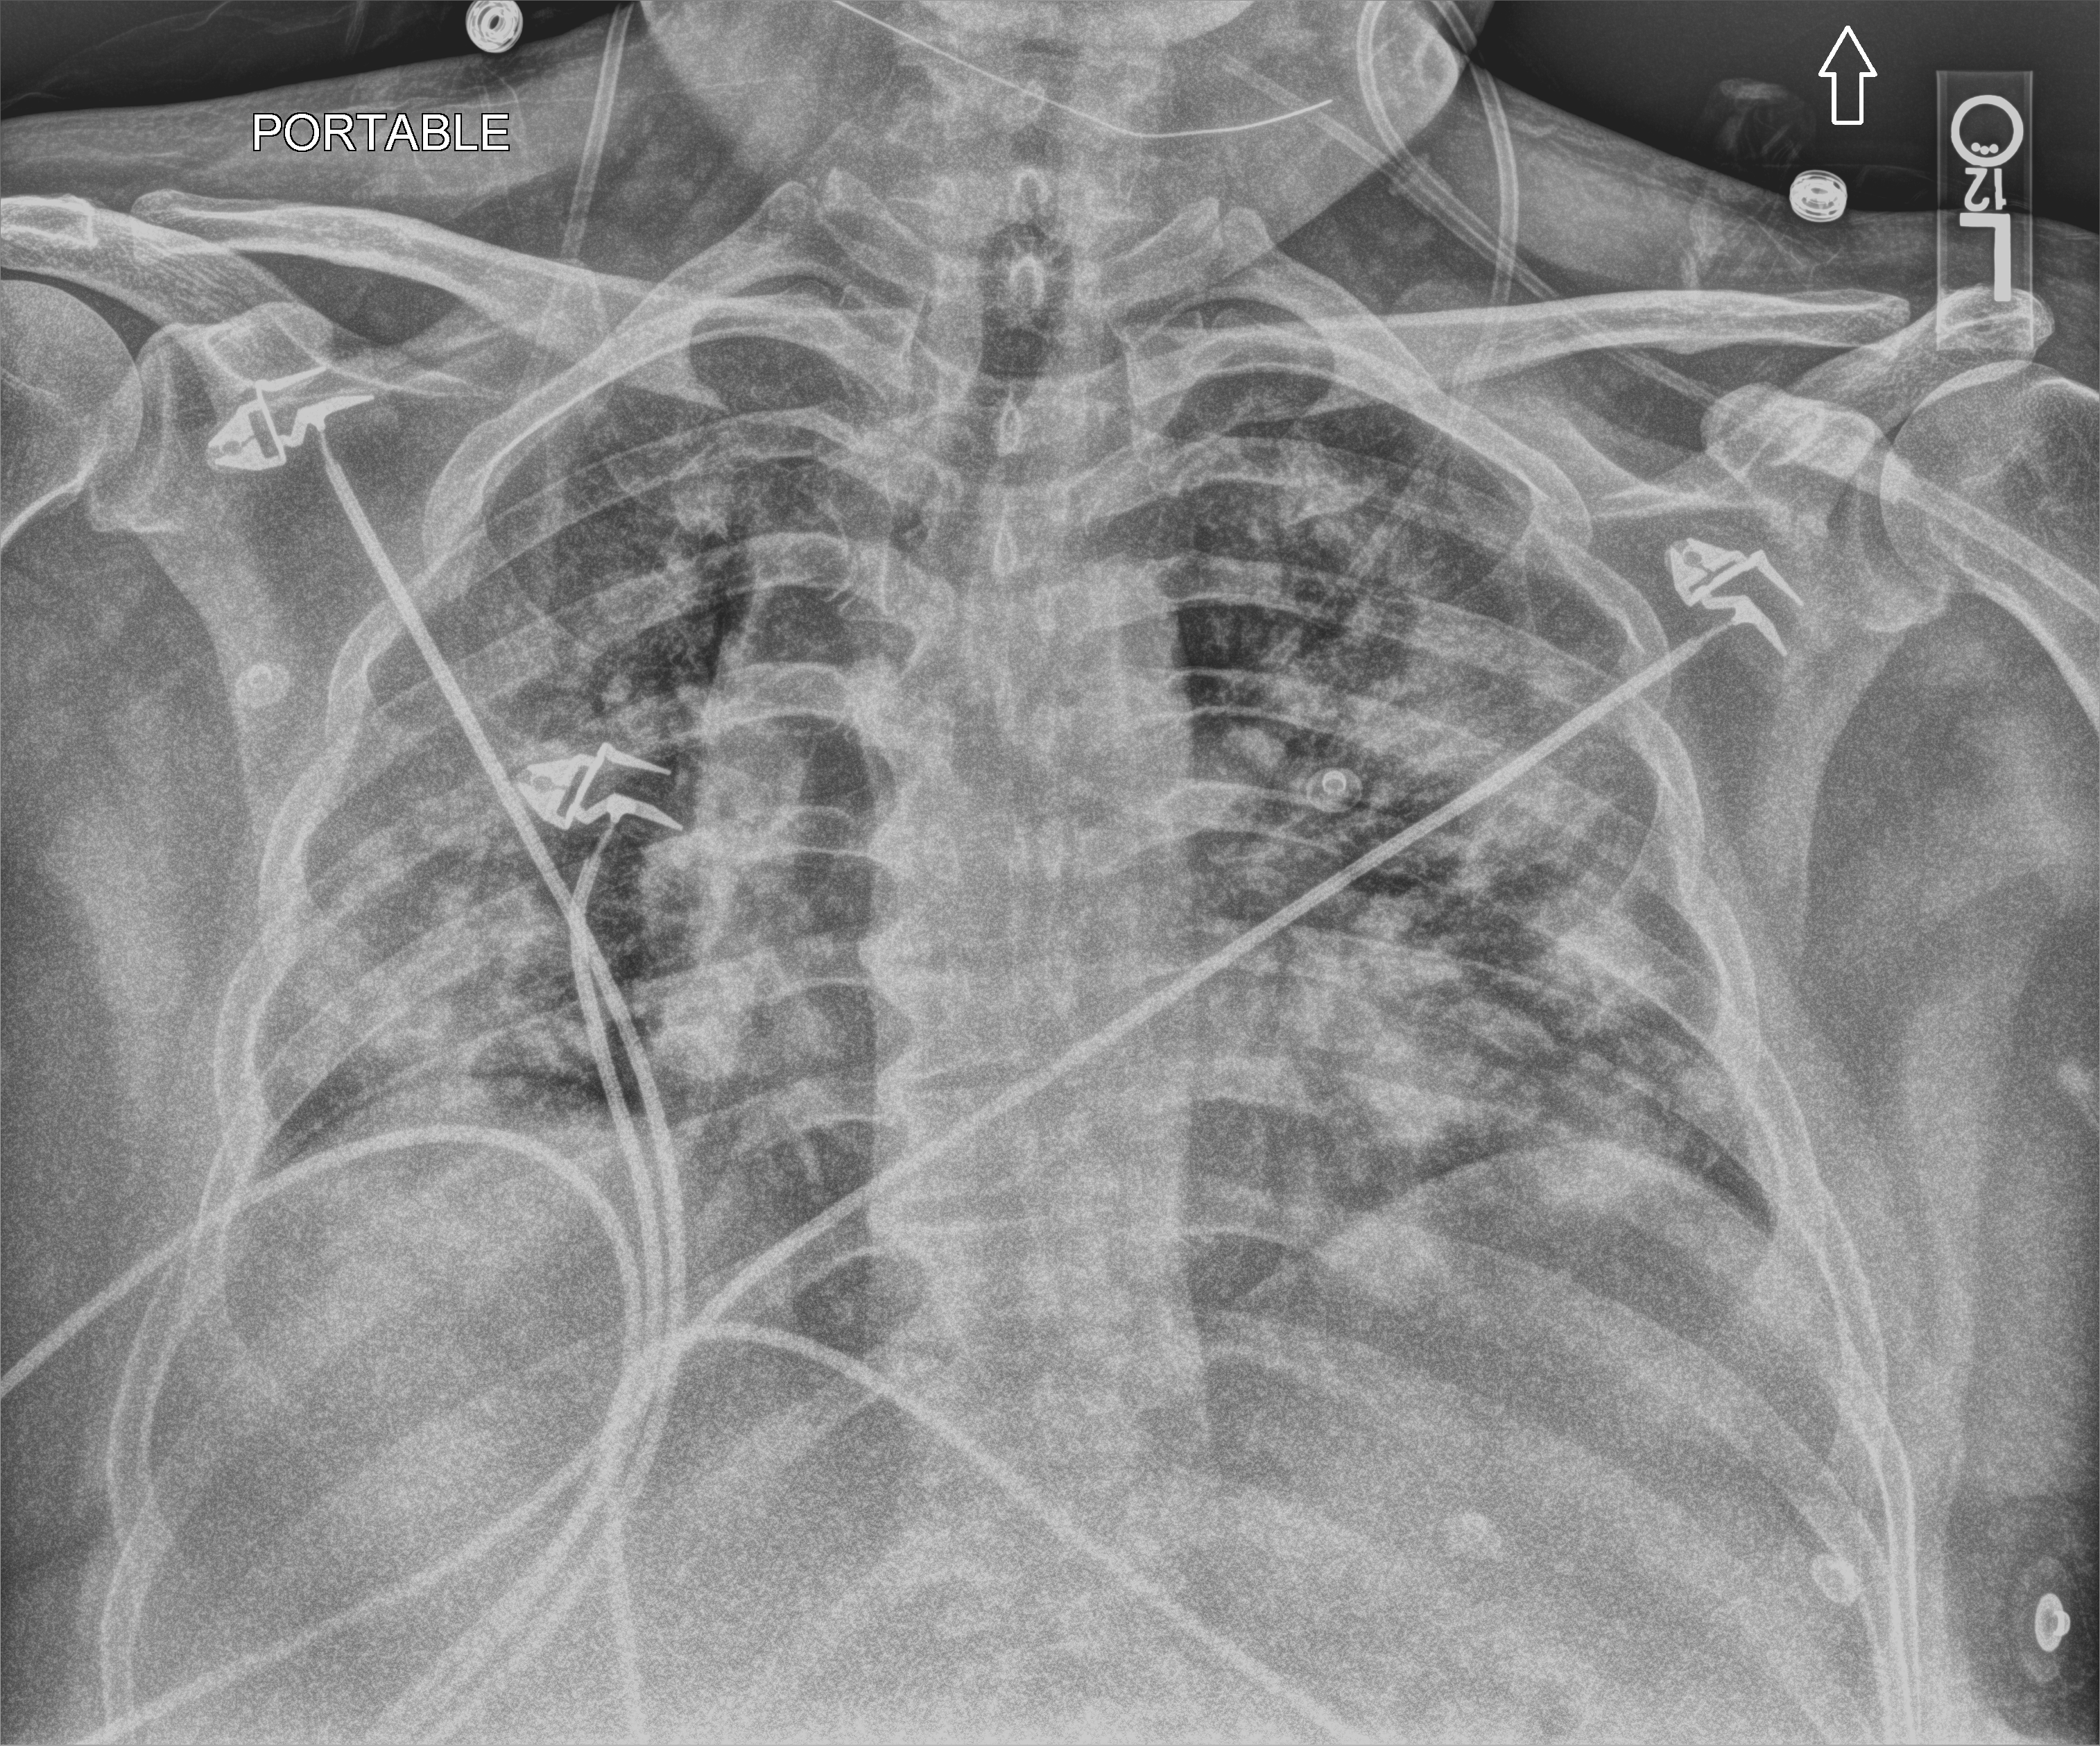
Portable chest radiograph. Patient hospitalised with COVID-19; male, aged 18–59 years.
From the hospital-stay record, not from the radiograph (when in the stay this image was taken is not recorded): admitted to intensive care during this hospital stay: yes; smoking status (admission record): never; hypertension (admission record): no.